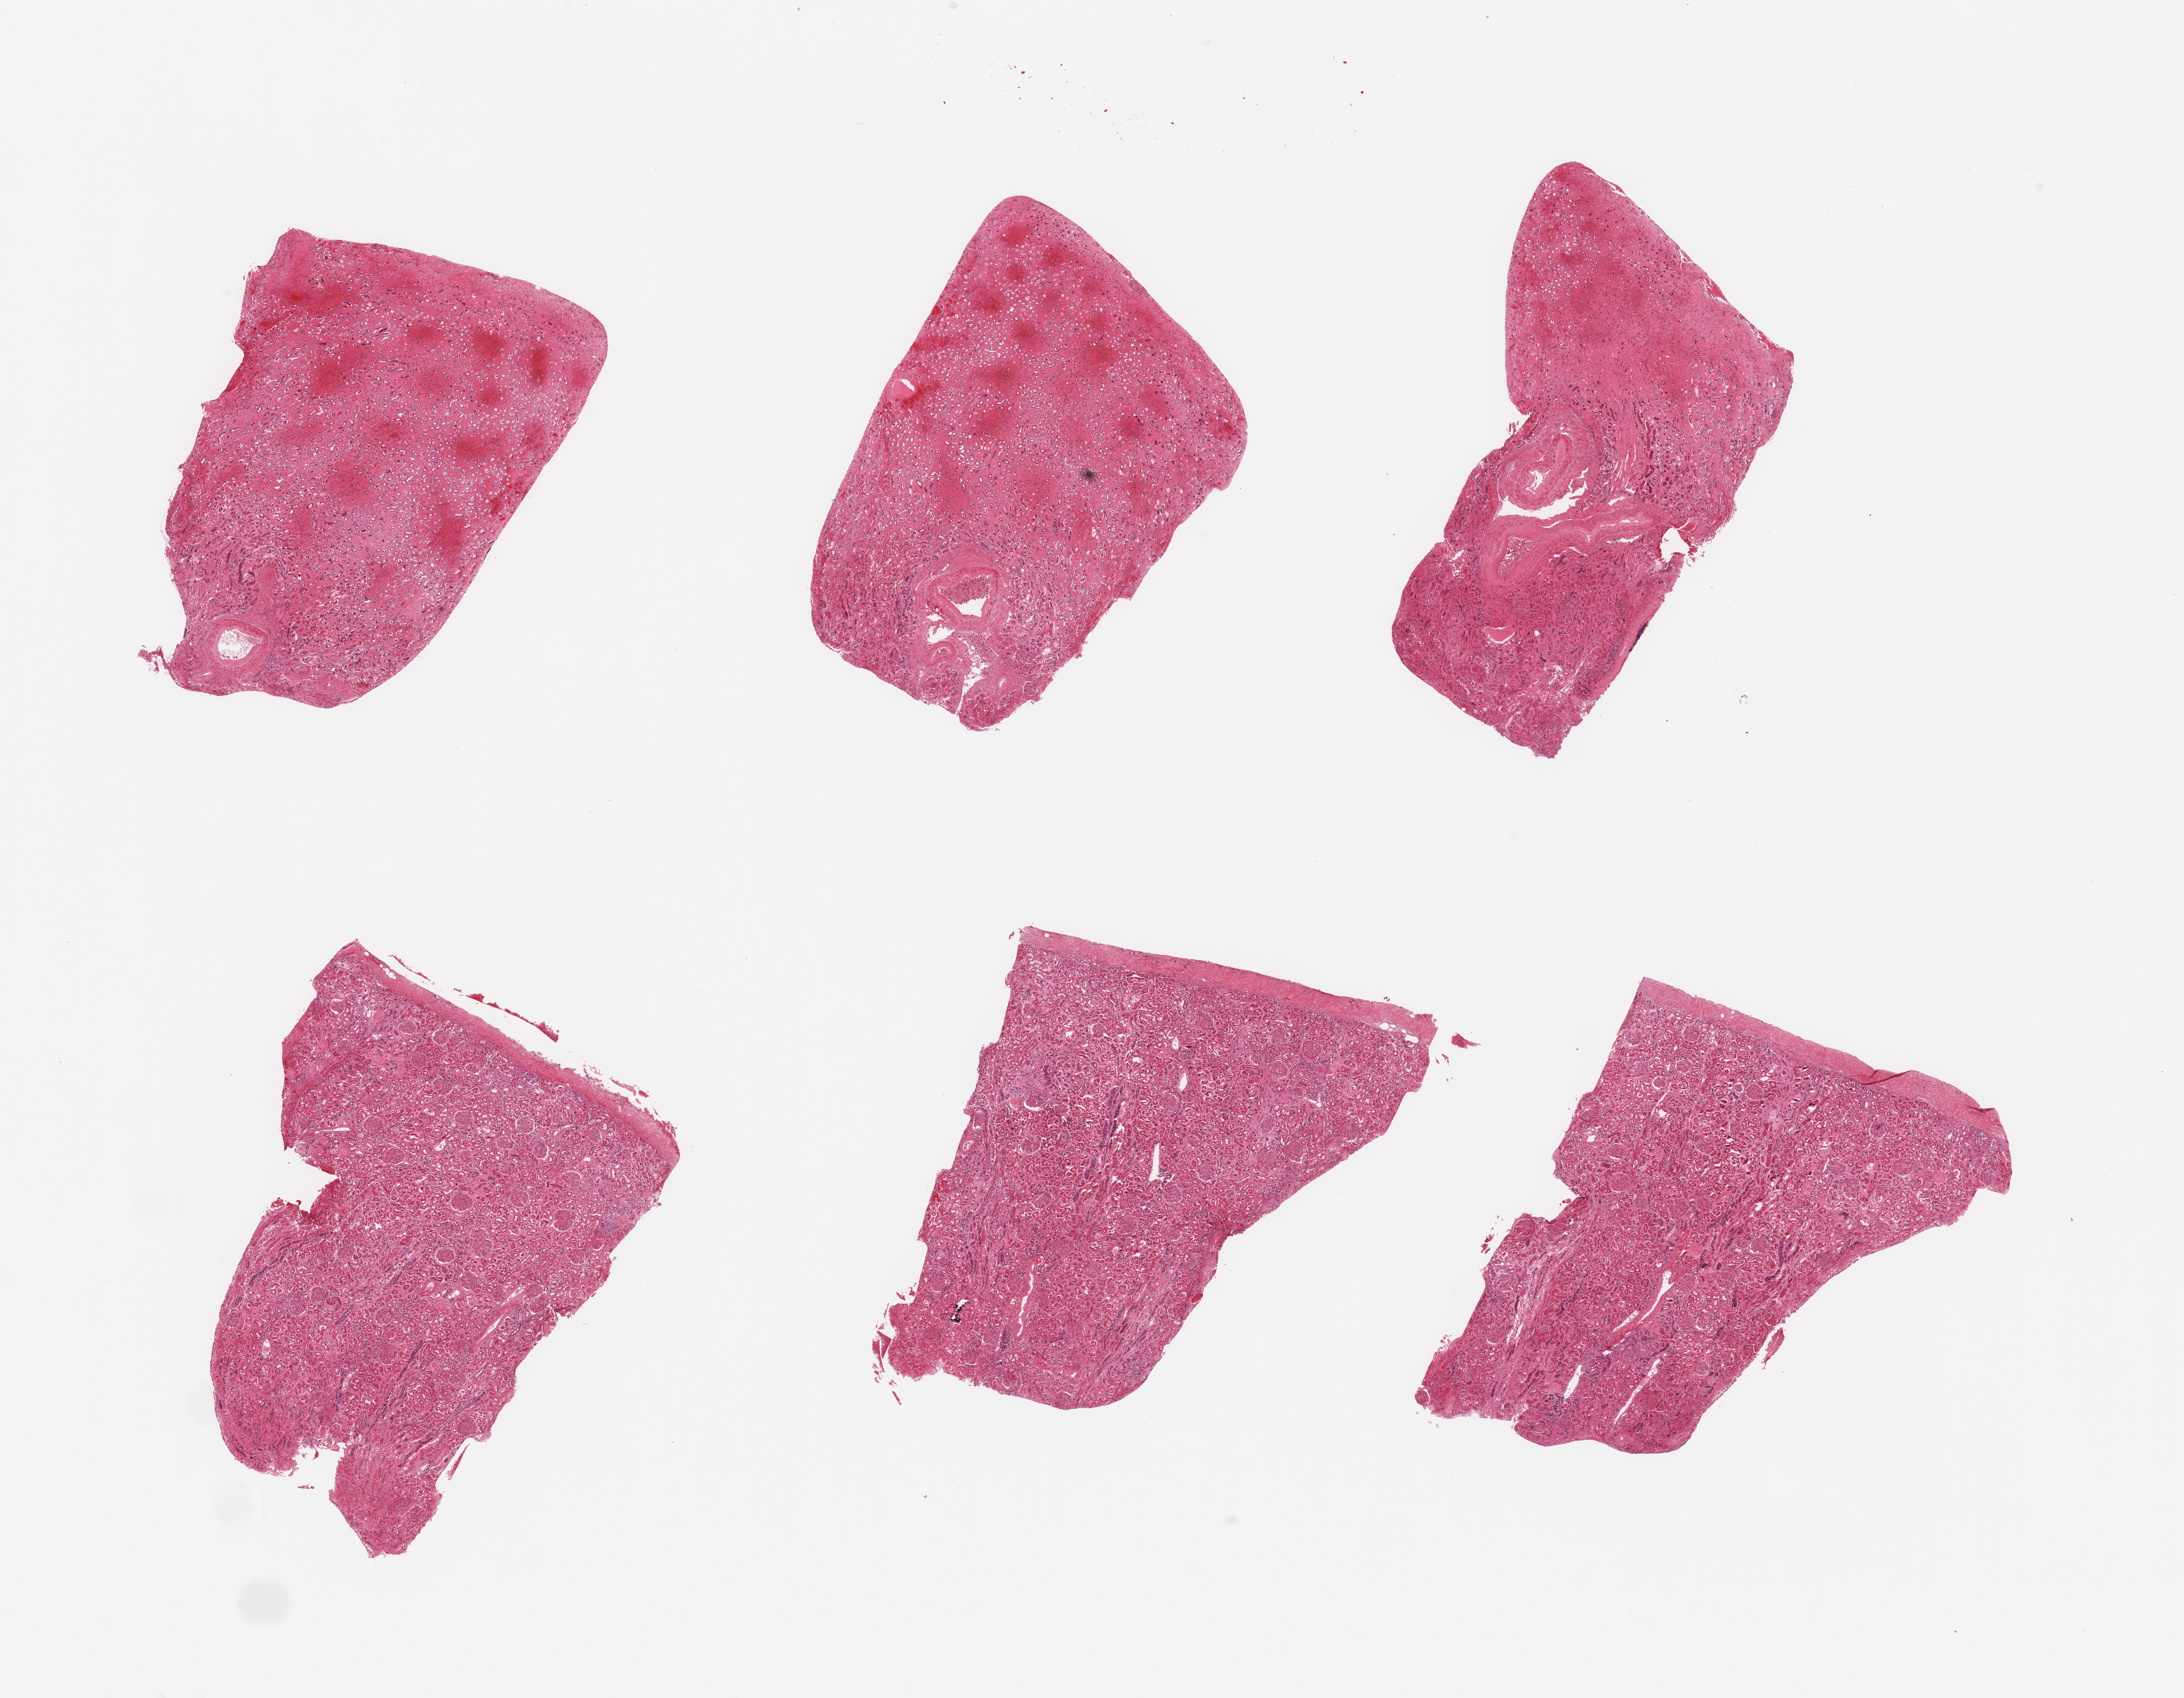
Digitized hematoxylin and eosin (H&E)-stained section — shown as a low-resolution overview of the whole scanned area (about 24.6 x 19.1 mm, from a 20x scan). PAXgene-fixed, paraffin-embedded tissue. Sampled site (target tissue): renal cortex. Donor tissue sample.
Review note (as recorded): 6 pieces: 3 are cortex, 3 are medulla.